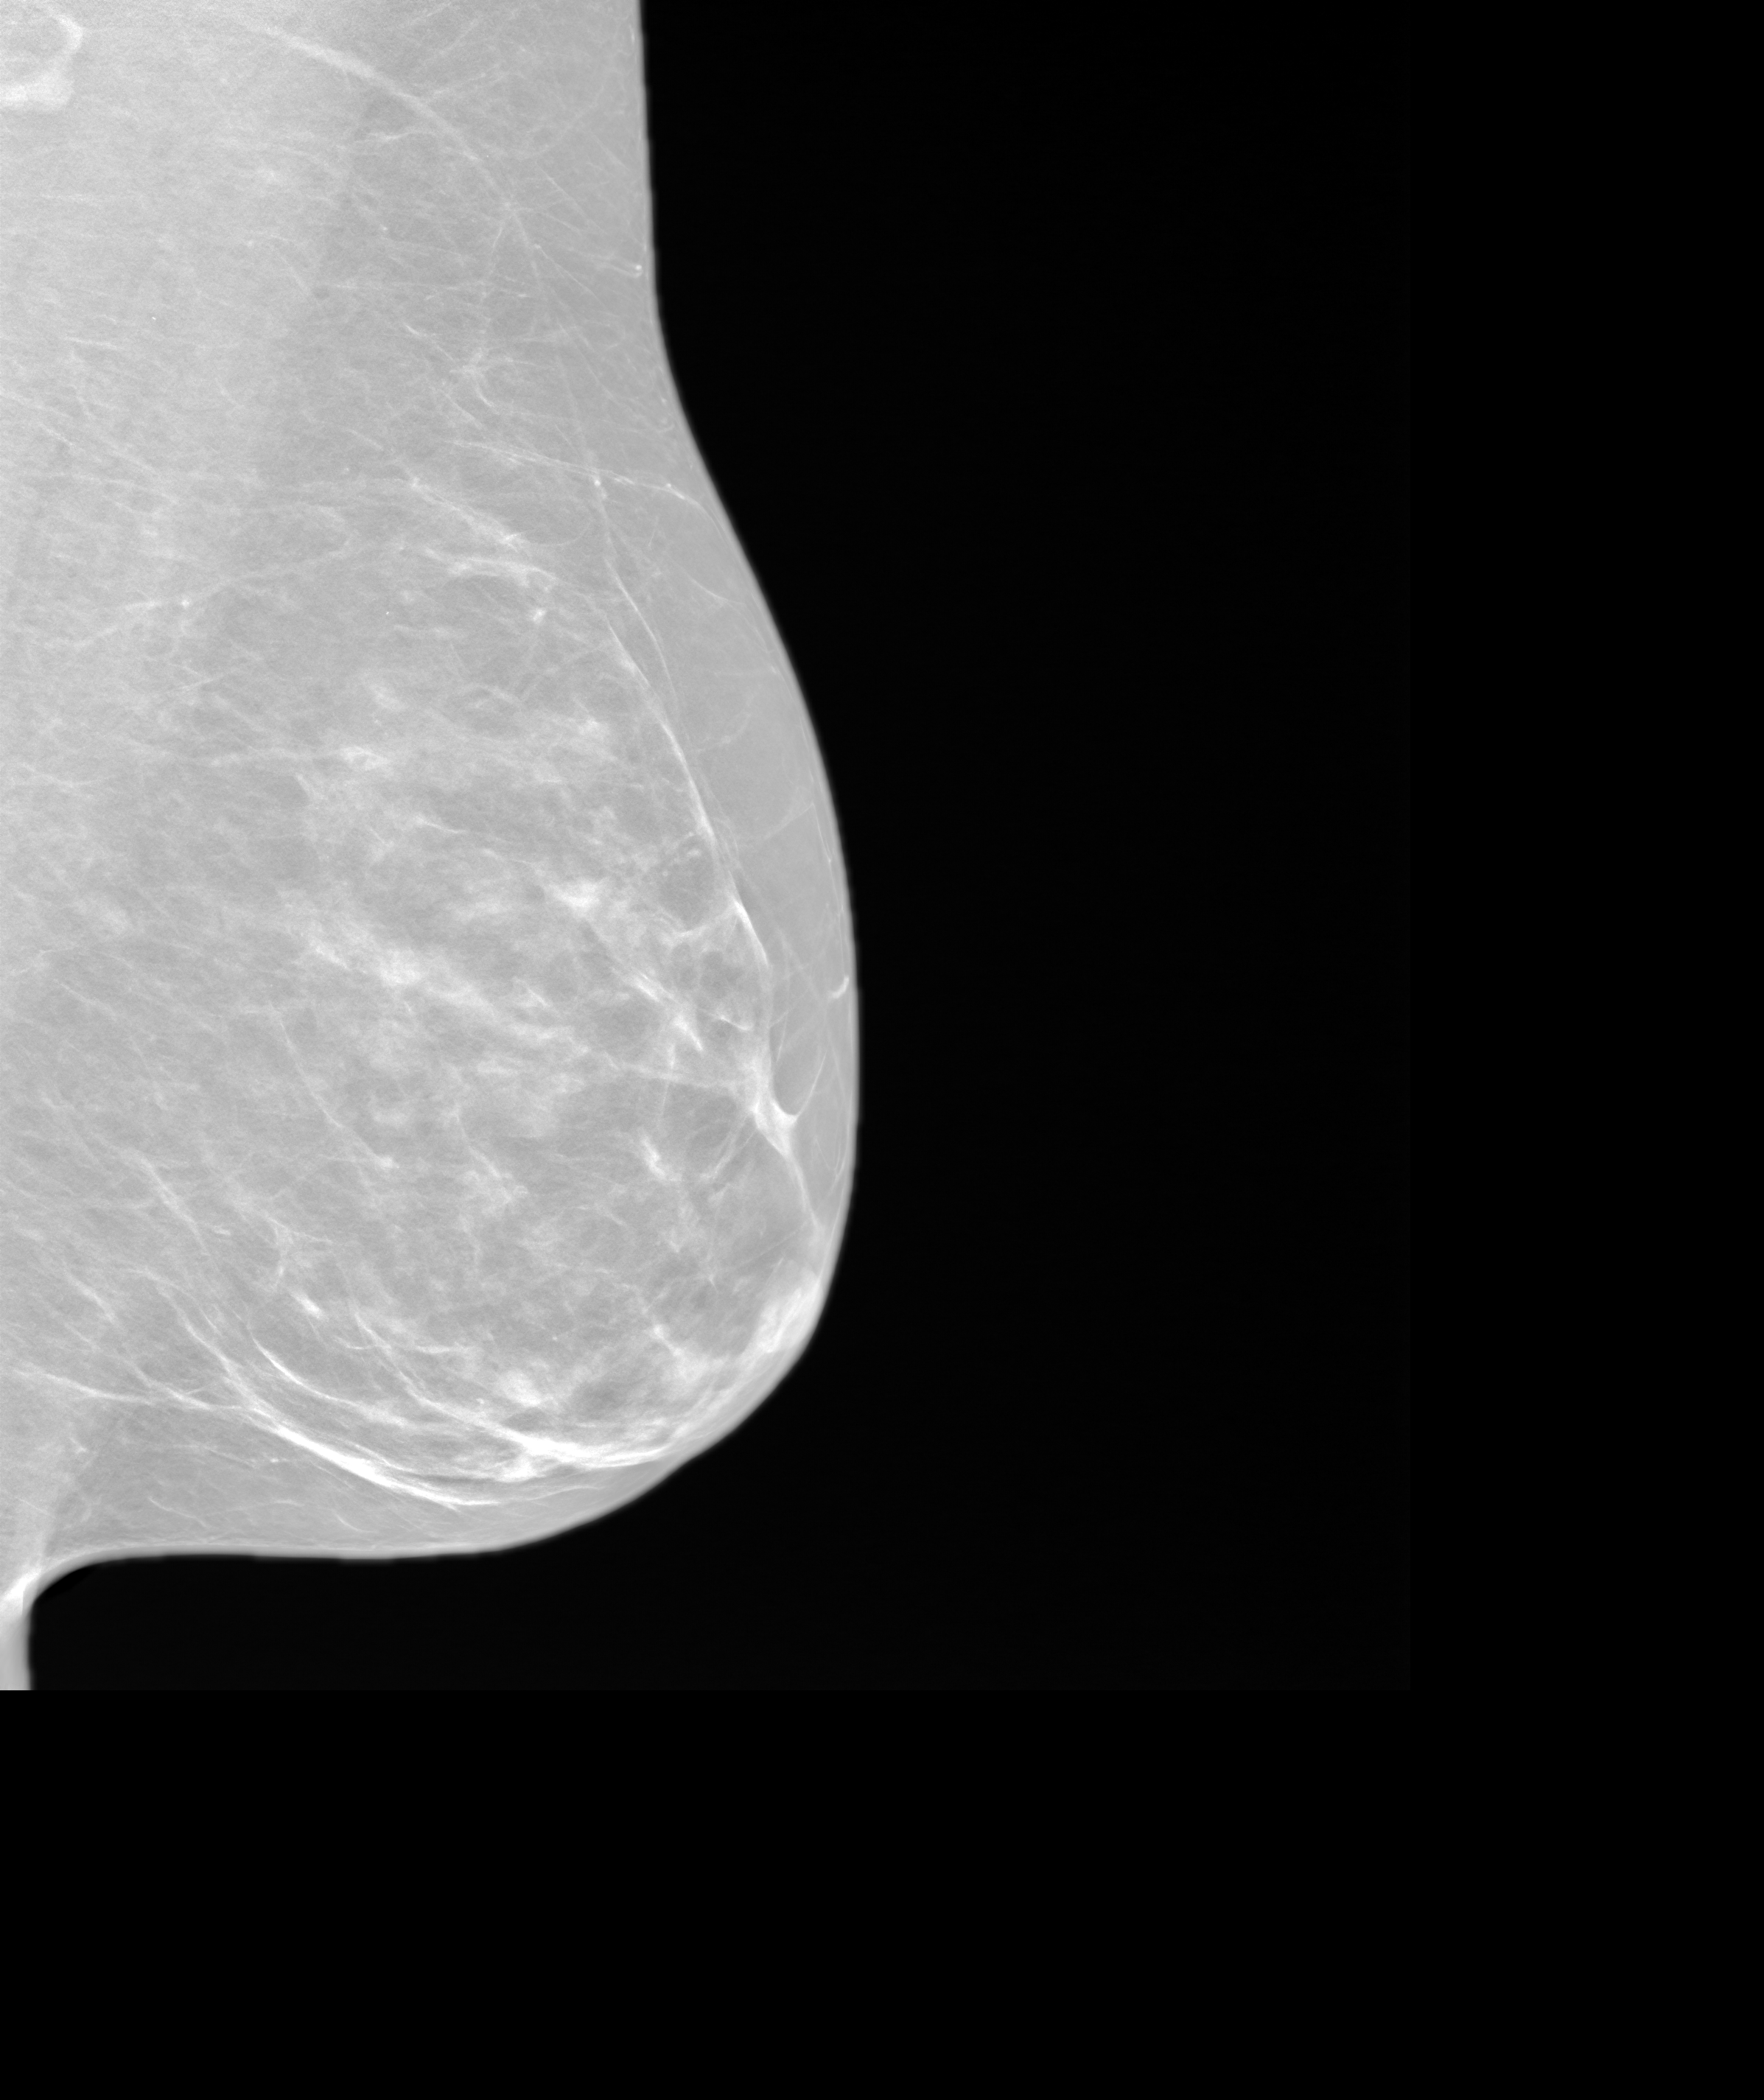
Screening examination. Patient: female, 58 years.
Image type: synthesized 2-D view from tomosynthesis. Breast: left. Projection: mediolateral oblique (MLO) view.